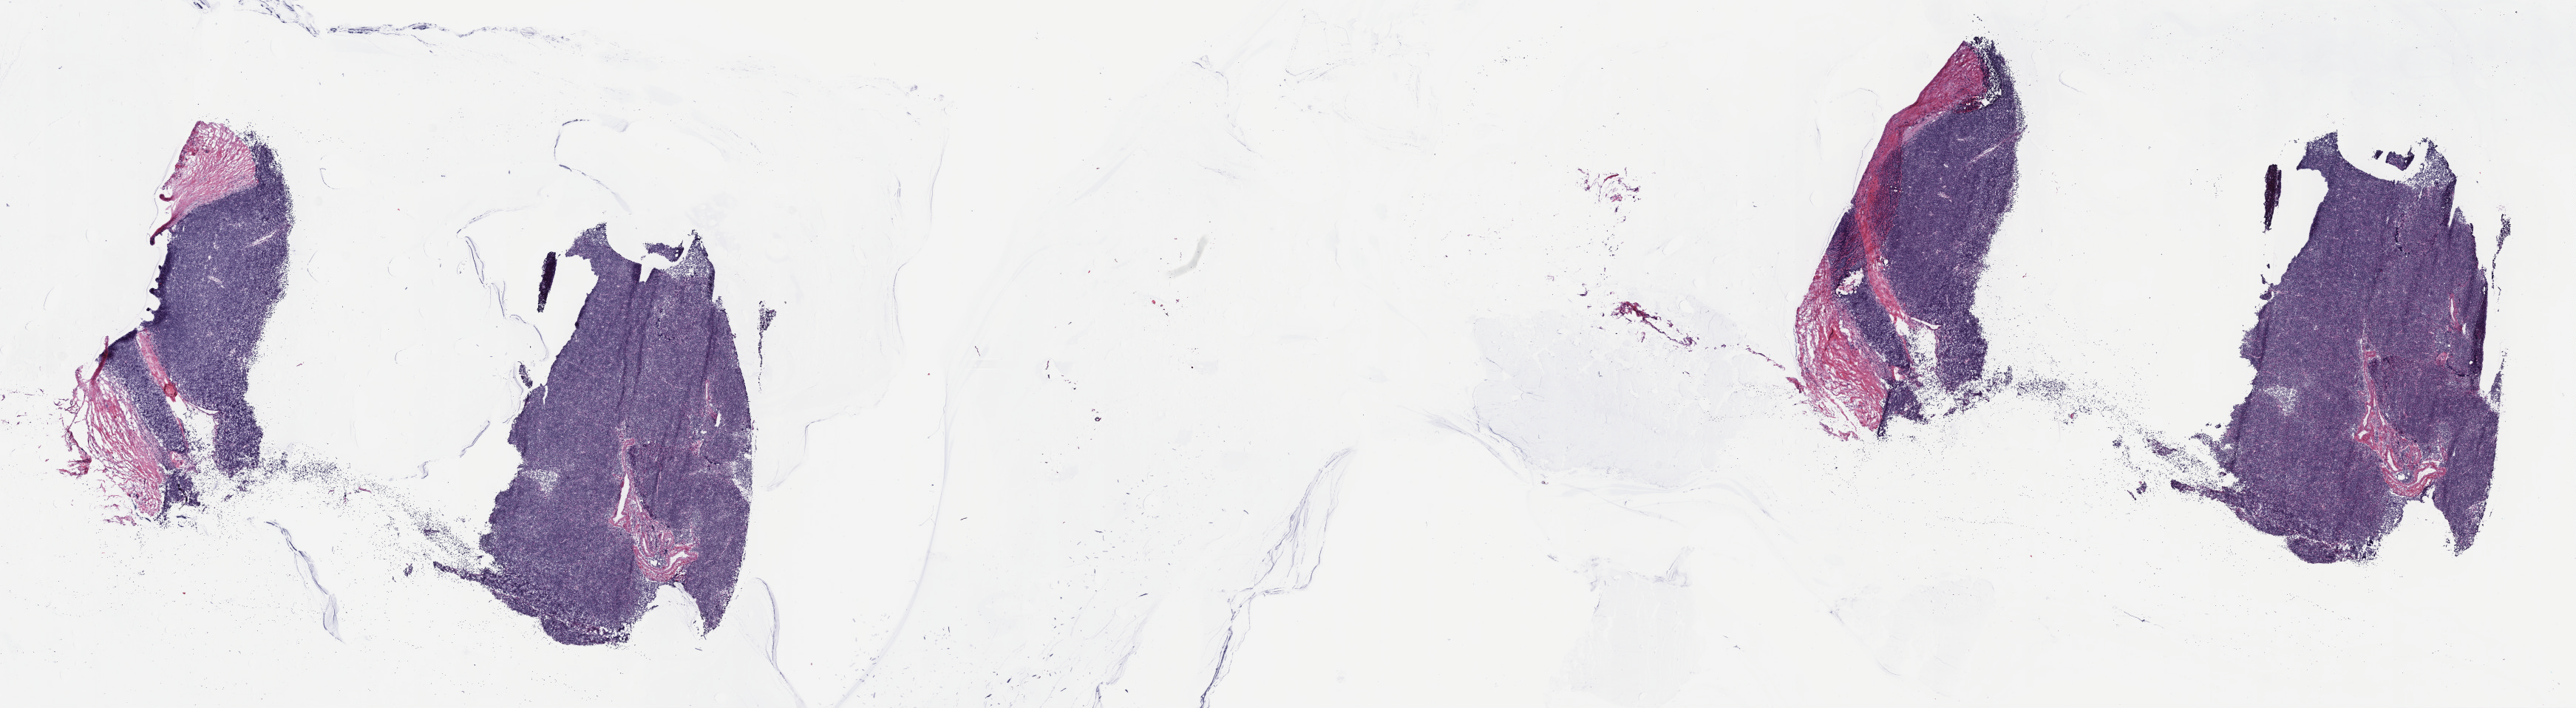
Whole-slide histology image, H&E-stained, a low-resolution overview of the entire scanned area, about 28.2 x 7.7 mm; frozen section; sample: primary tumour, thymus. Male patient; age at initial diagnosis 47 years. Composition of this section per pathologist review: tumour cells 80%, tumour nuclei 90%, normal cells 0%, stromal cells 20%, necrosis 0%. Infiltration values recorded for this section: lymphocyte infiltration 0%, monocyte infiltration 0%, neutrophil infiltration 0%.
Pathologic diagnosis: Thymoma, type B1, malignant.